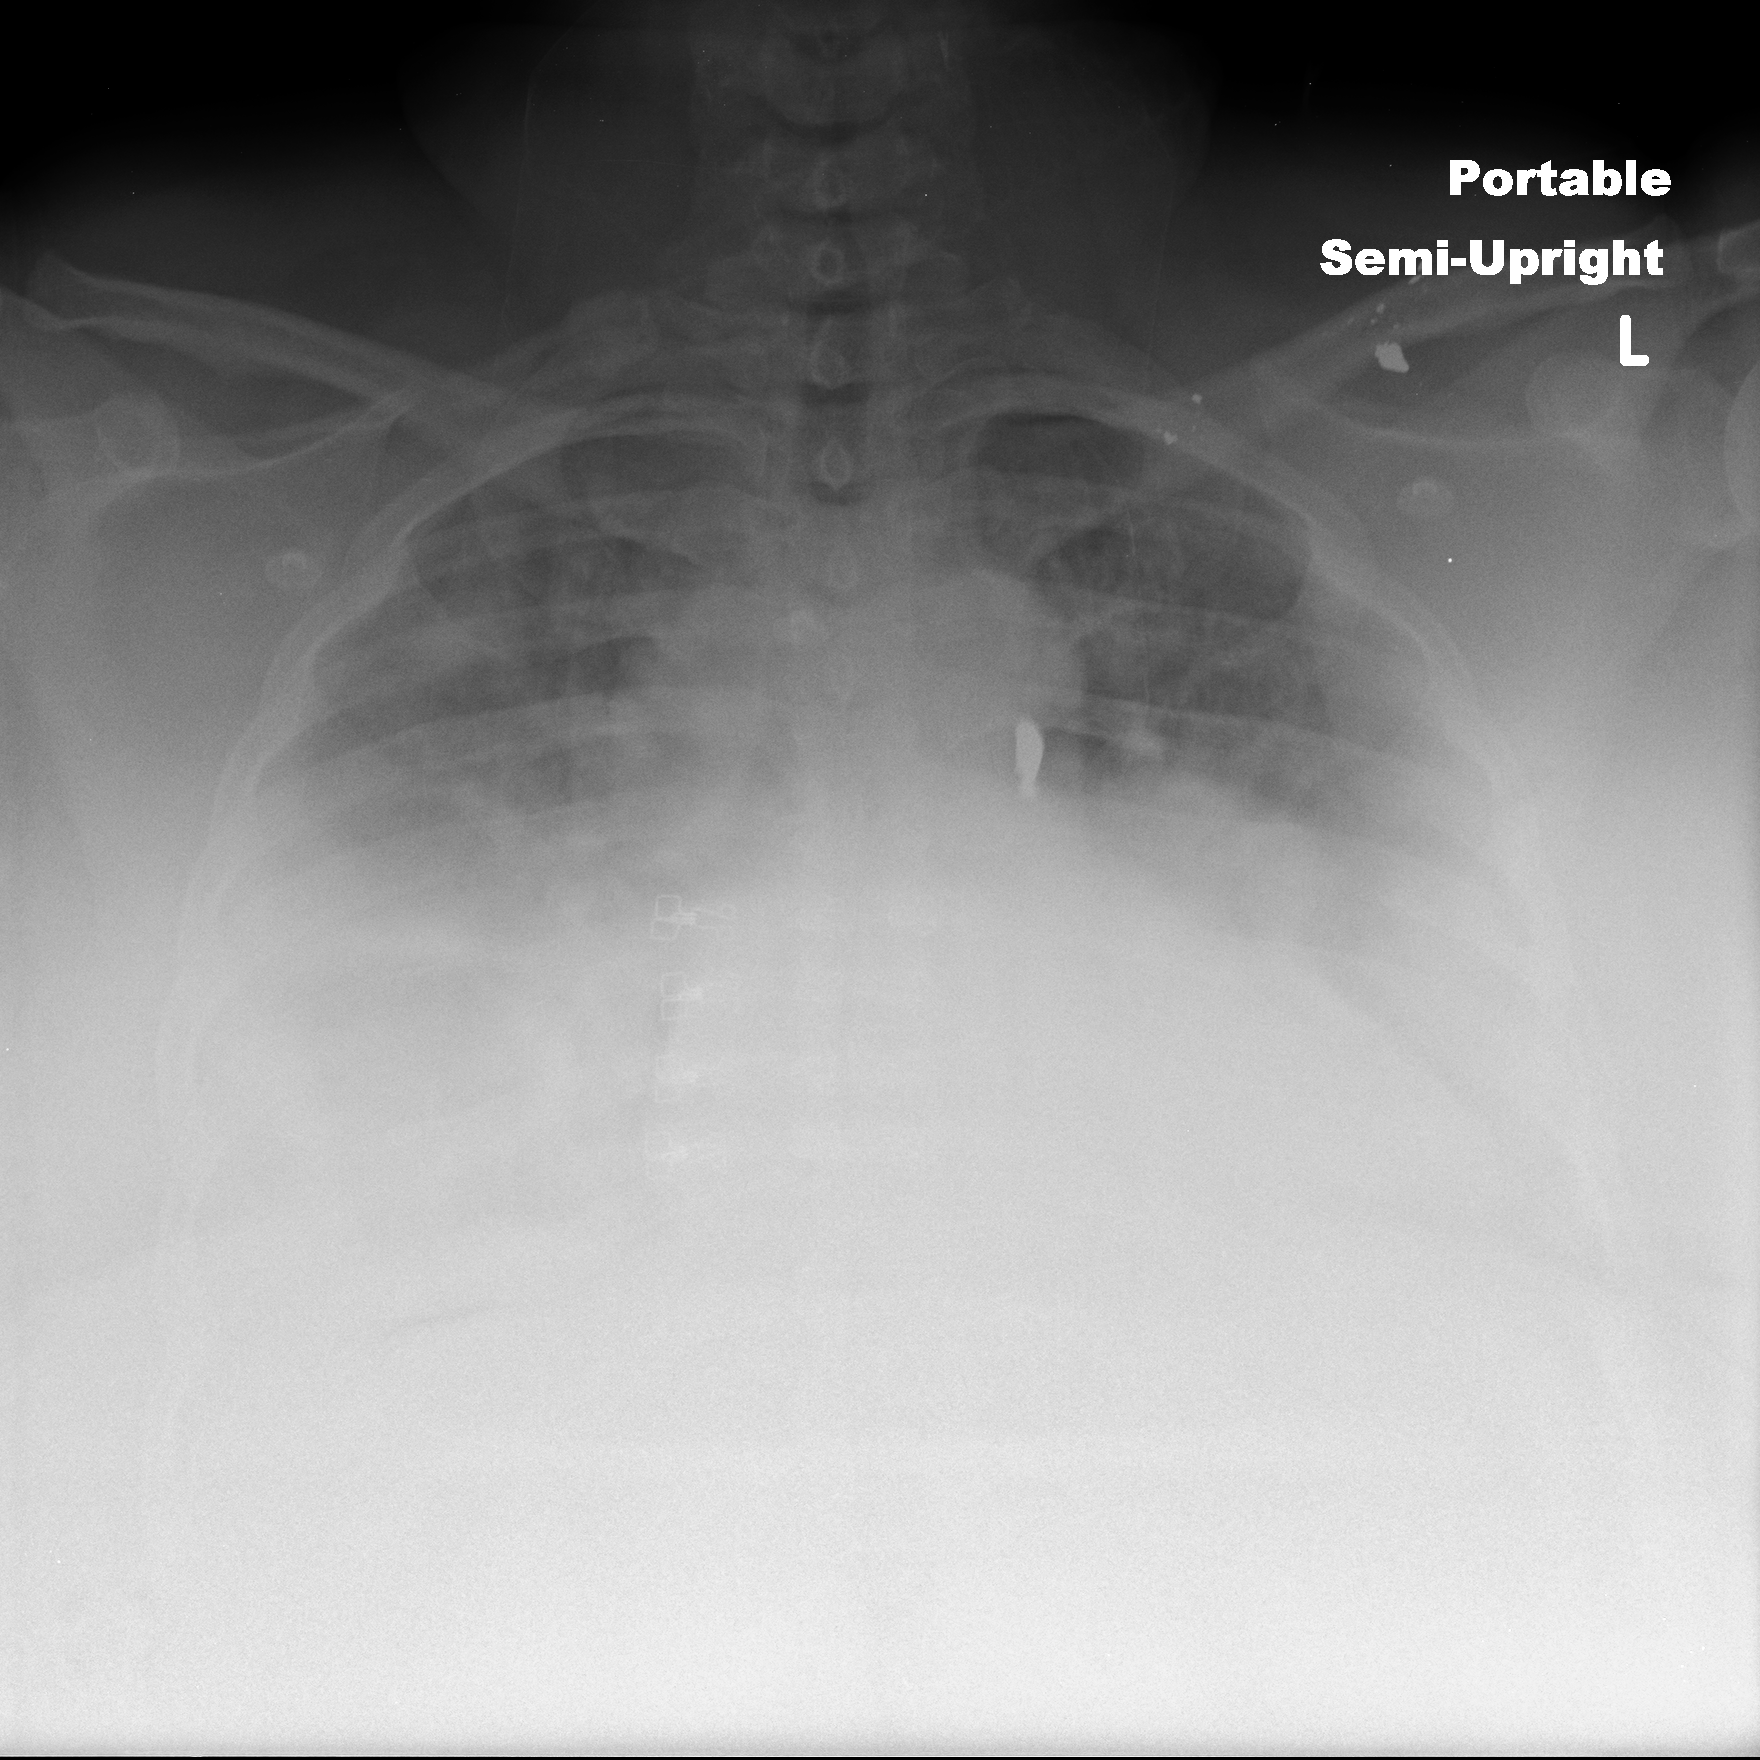
Chest X-ray (portable), AP projection. Female patient, age 42 years; imaged 3 days after the COVID-19 diagnosis.
Radiologist key findings (as recorded): There has been interval worsening of the diffuse opacities throughout the lung bases.